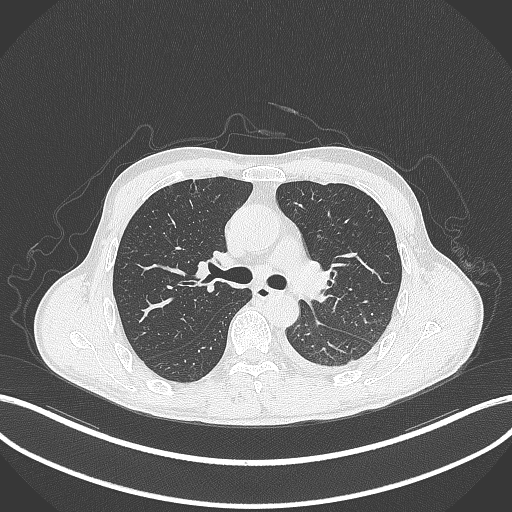
Chest CT, one axial slice; position 211 of 295 along the scan axis; 120 kVp; lung window (W 1500 / L -600 HU); 1 mm slice thickness; 512 × 512 image matrix. Male patient, age 47 years. Case-level facts recorded for this patient, not image findings: clinical TNM (as recorded): T3 N1 M1c; histopathological grade: G3.
Outlined on this slice (rectangle marked by the reading radiologist):
- lung tumour (recorded histology: small cell carcinoma): bounding box <303,280,327,304> (left, top, right, bottom; pixels)